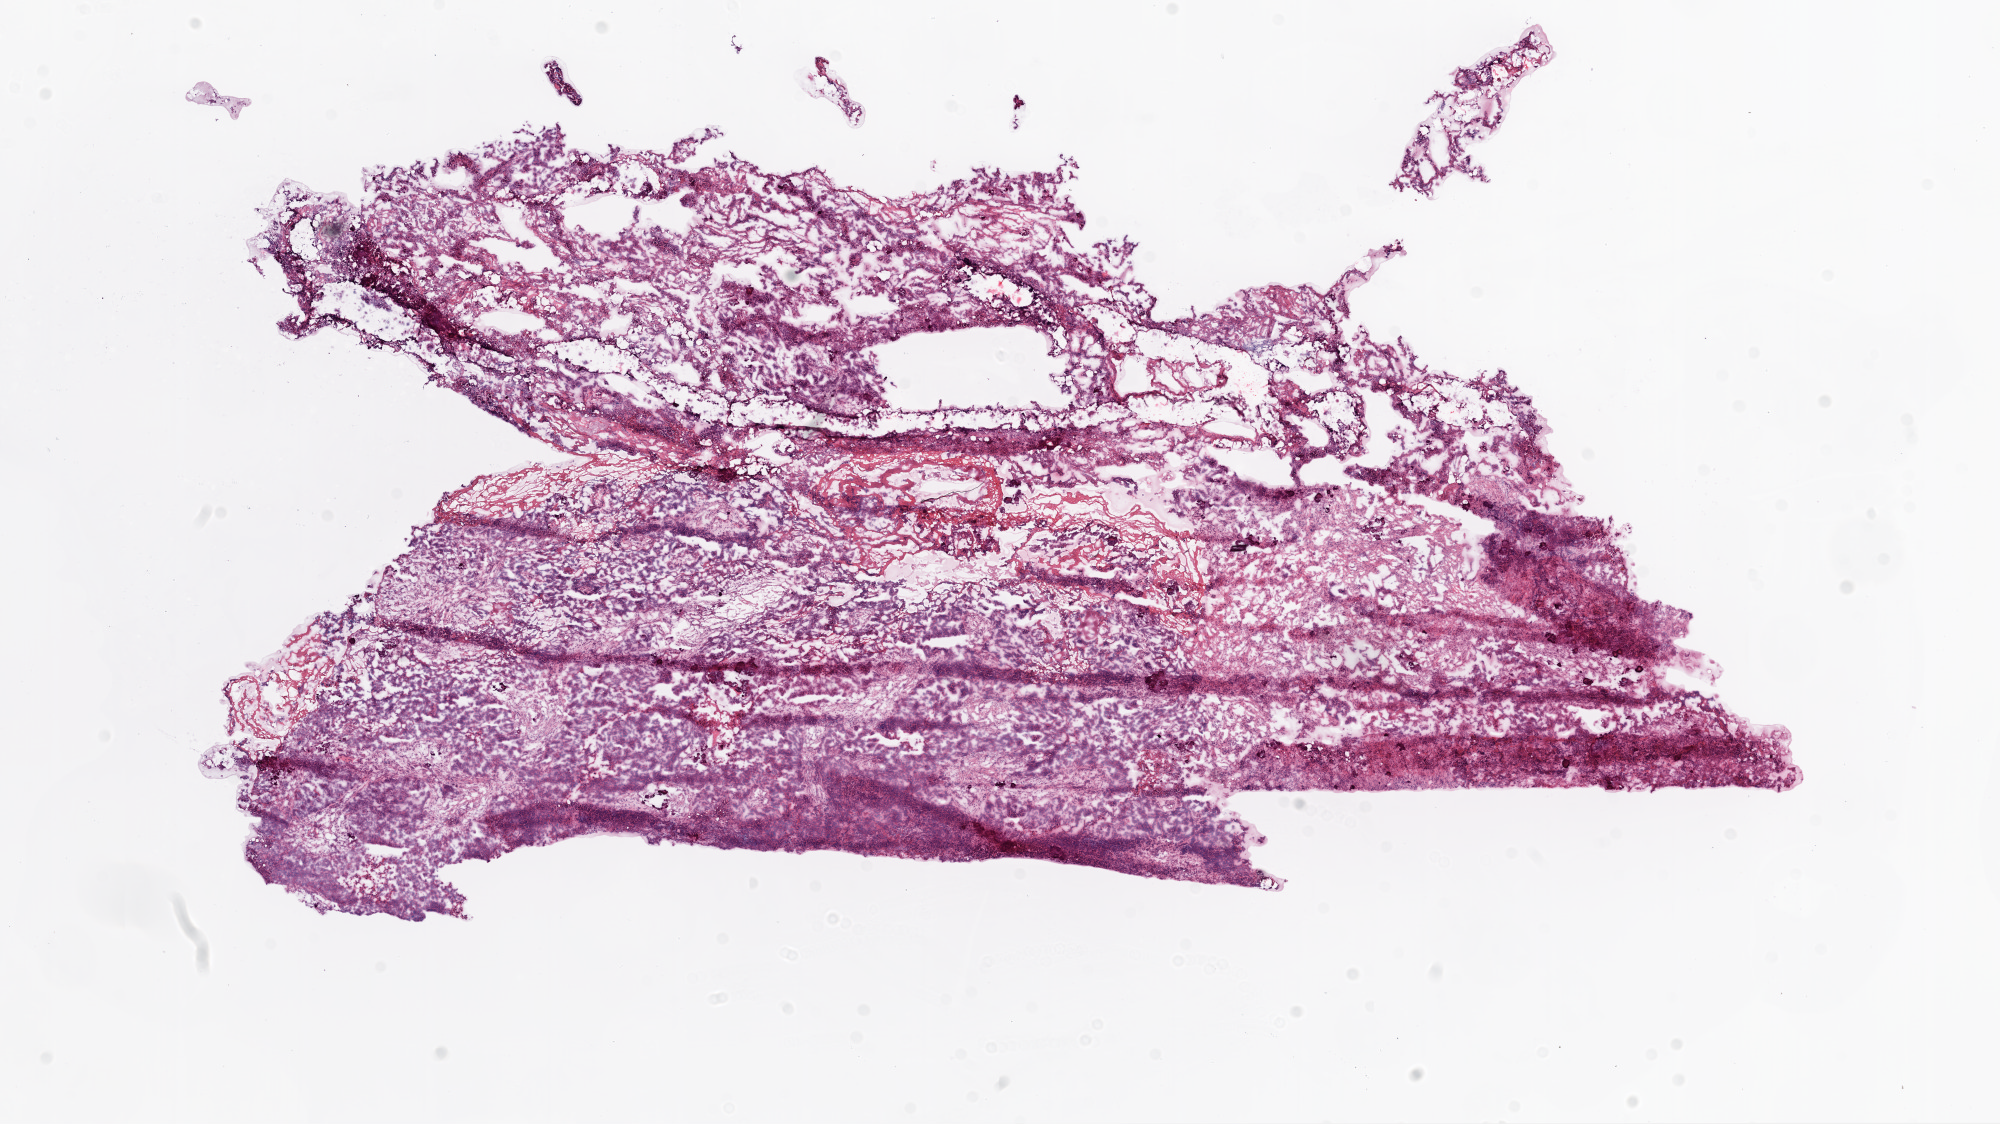
Whole-slide histology image, H&E-stained — whole scanned area (about 16.0 x 9.0 mm, from a 20x scan) shown as a low-resolution overview. Frozen section. Ovary, primary tumour sample. Patient: female, age at initial diagnosis 74 years.
Histologic diagnosis: Serous cystadenocarcinoma, NOS.